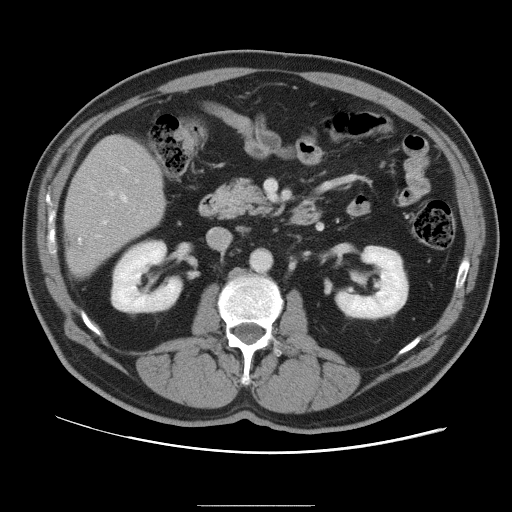
Contrast-enhanced abdominal CT, one axial slice. Position 40 of 105 along the scan axis. 120 kVp. Intravenous contrast given. Soft-tissue window (W 400 / L 40 HU). 512 × 512 image matrix. Male patient, age 64 years. From the clinical record (not read from this slice): diagnosis: colorectal cancer liver metastases, imaged before liver resection; multiple liver metastases: yes; largest metastasis: 3 cm.
Annotated regions visible in this slice (manually delineated by an expert):
- hepatic veins: bounding box <103,195,127,224> (left, top, right, bottom; pixels)
- liver: <66,136,166,276>
- planned liver remnant (the part of the liver to remain after resection): <67,136,165,250>
- portal vein (with intrahepatic branches): <98,167,128,237>
- liver metastasis: <69,232,86,254>